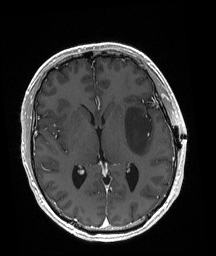
Brain MRI from a brain-tumour surgery series, one axial slice. Slice 99 of 192 in the series (ordered by position). T1-weighted post-contrast. 1 mm slice thickness. 216 × 256 image matrix, field of view 211 × 250 mm. Case-level facts recorded for this patient, not image findings: histopathology: Astrocytoma; WHO grade: 3; IDH mutation: yes; tumour location: Left Posterior Frontal.
Structures marked on this image (outlined manually by an expert reader):
- tumour: bounding box (x1, y1, x2, y2) in pixels: (124, 106, 152, 156)